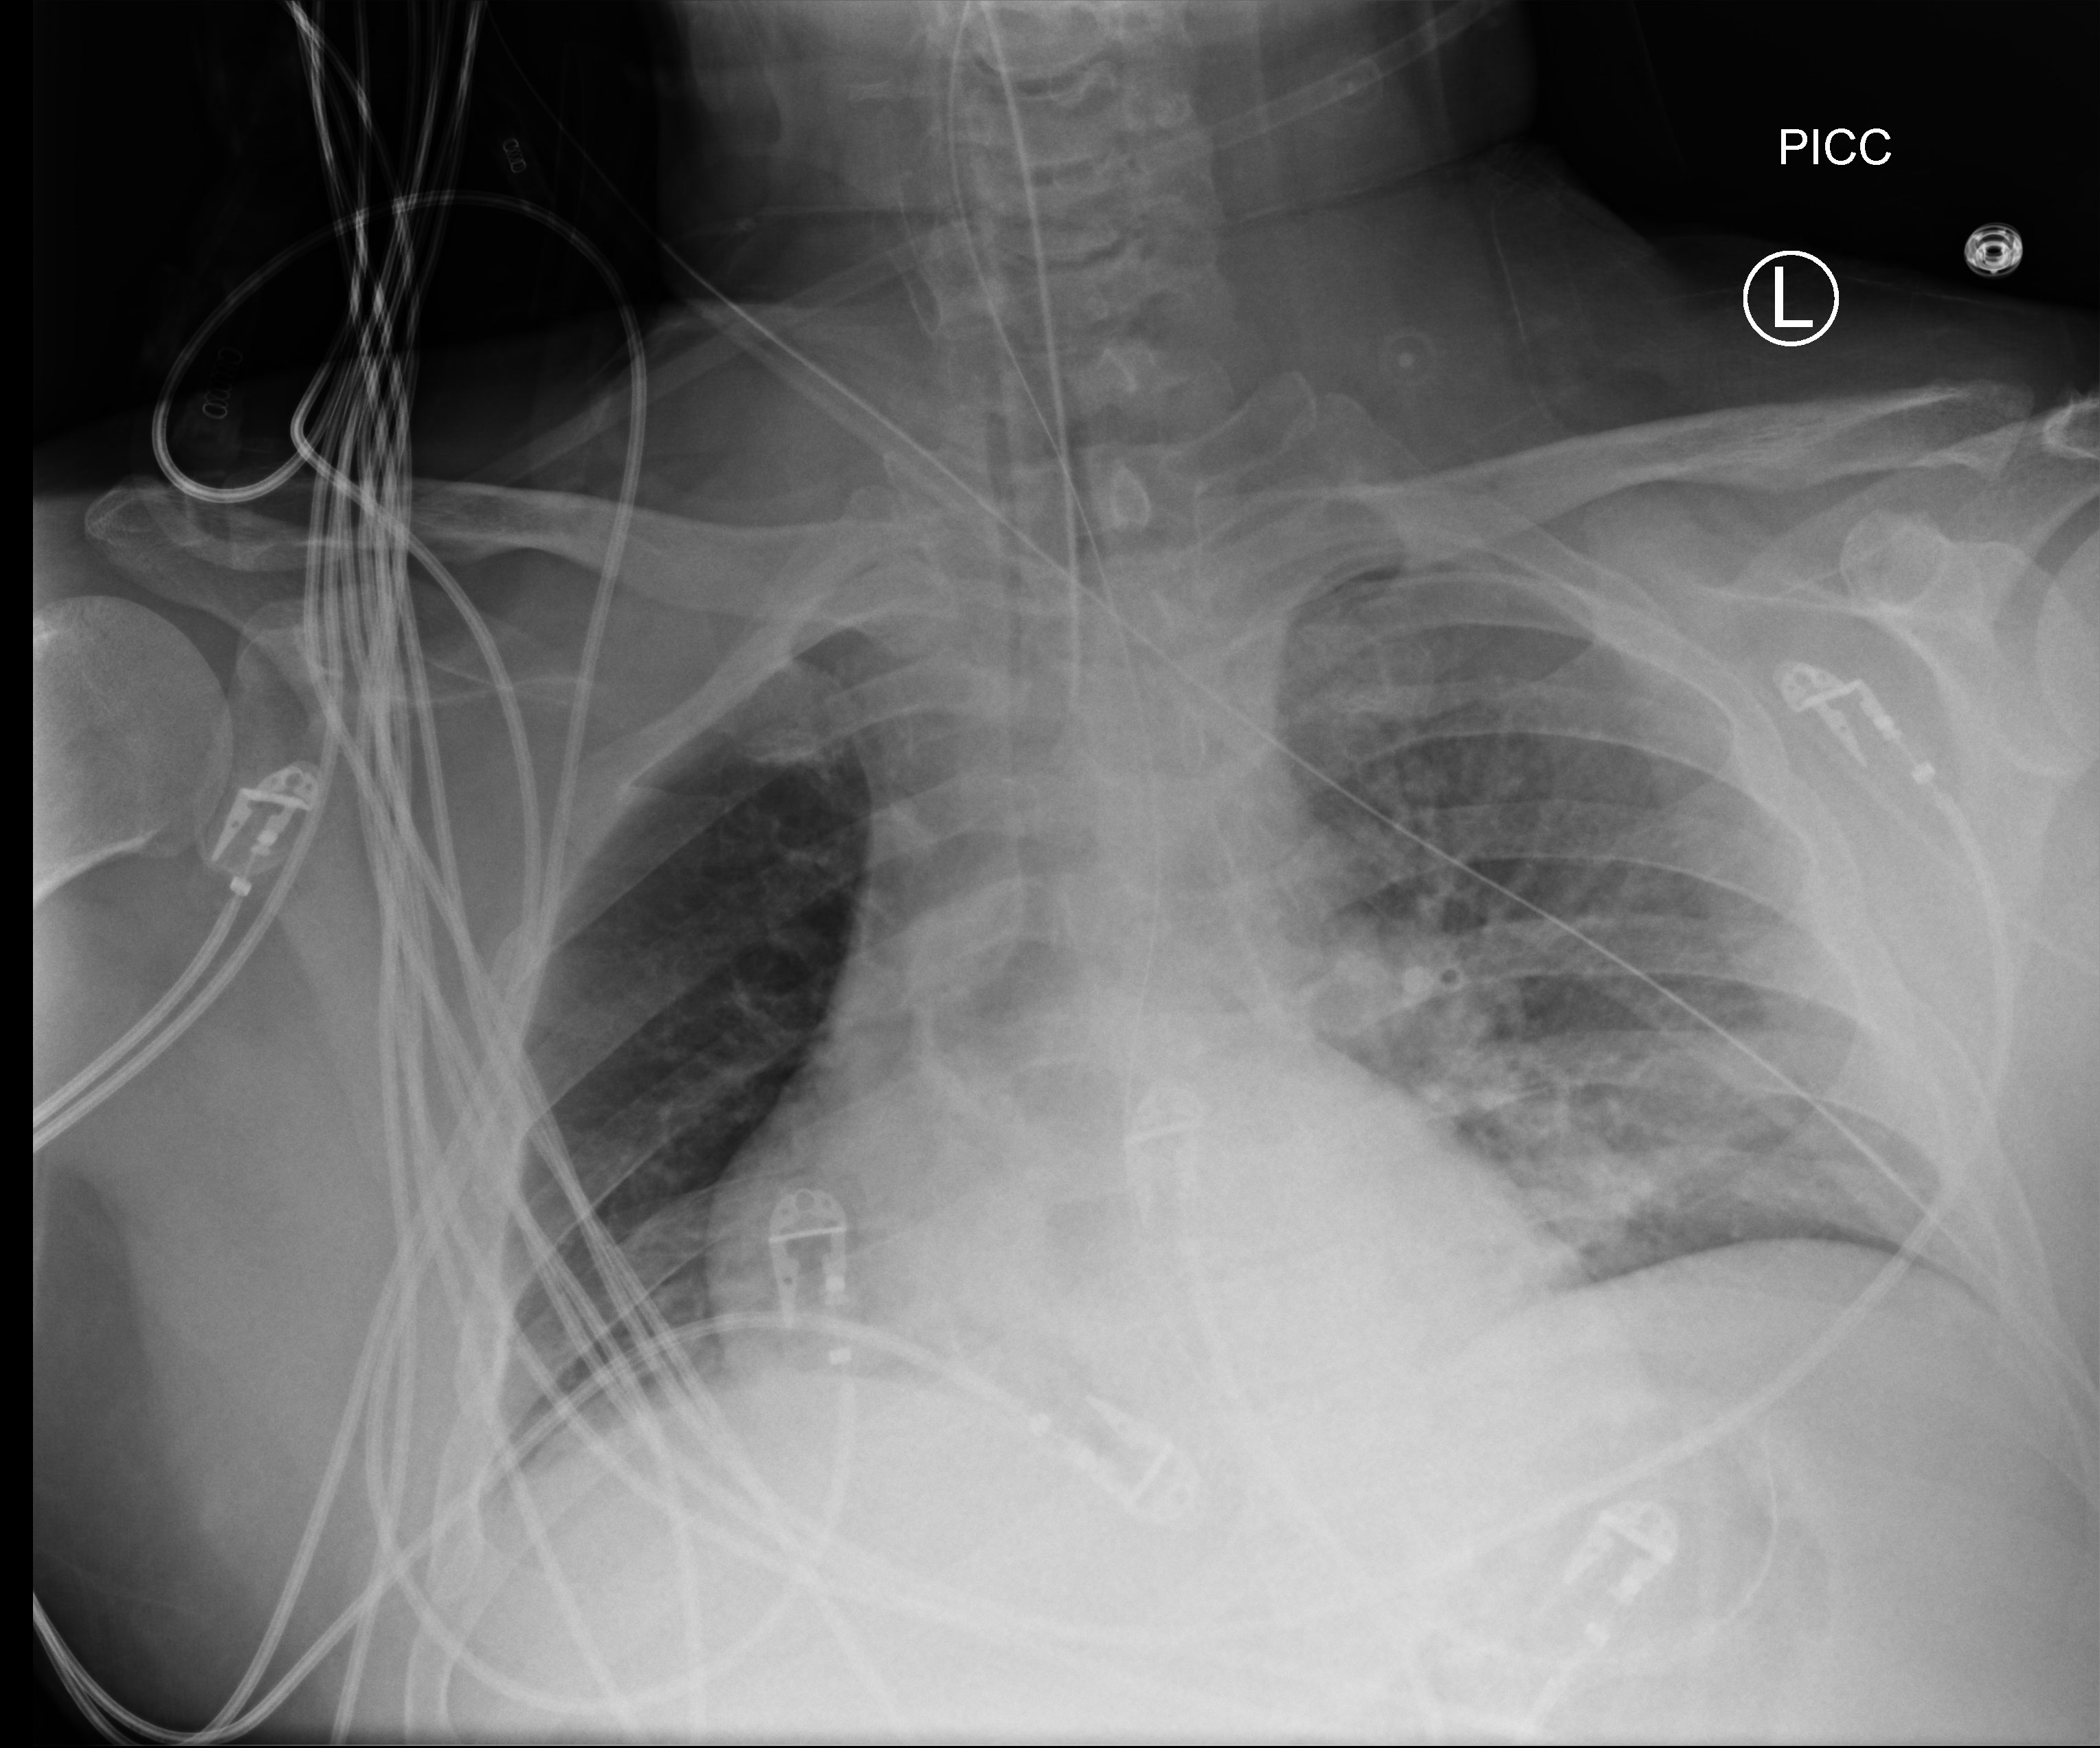
Bedside chest radiograph (computed radiography); anteroposterior (AP) projection. Male patient hospitalised with COVID-19, age 18–59 years.
From the hospital-stay record, not from the radiograph (when in the stay this image was taken is not recorded):
- admitted to intensive care during this hospital stay: yes
- mechanically ventilated during this hospital stay: yes